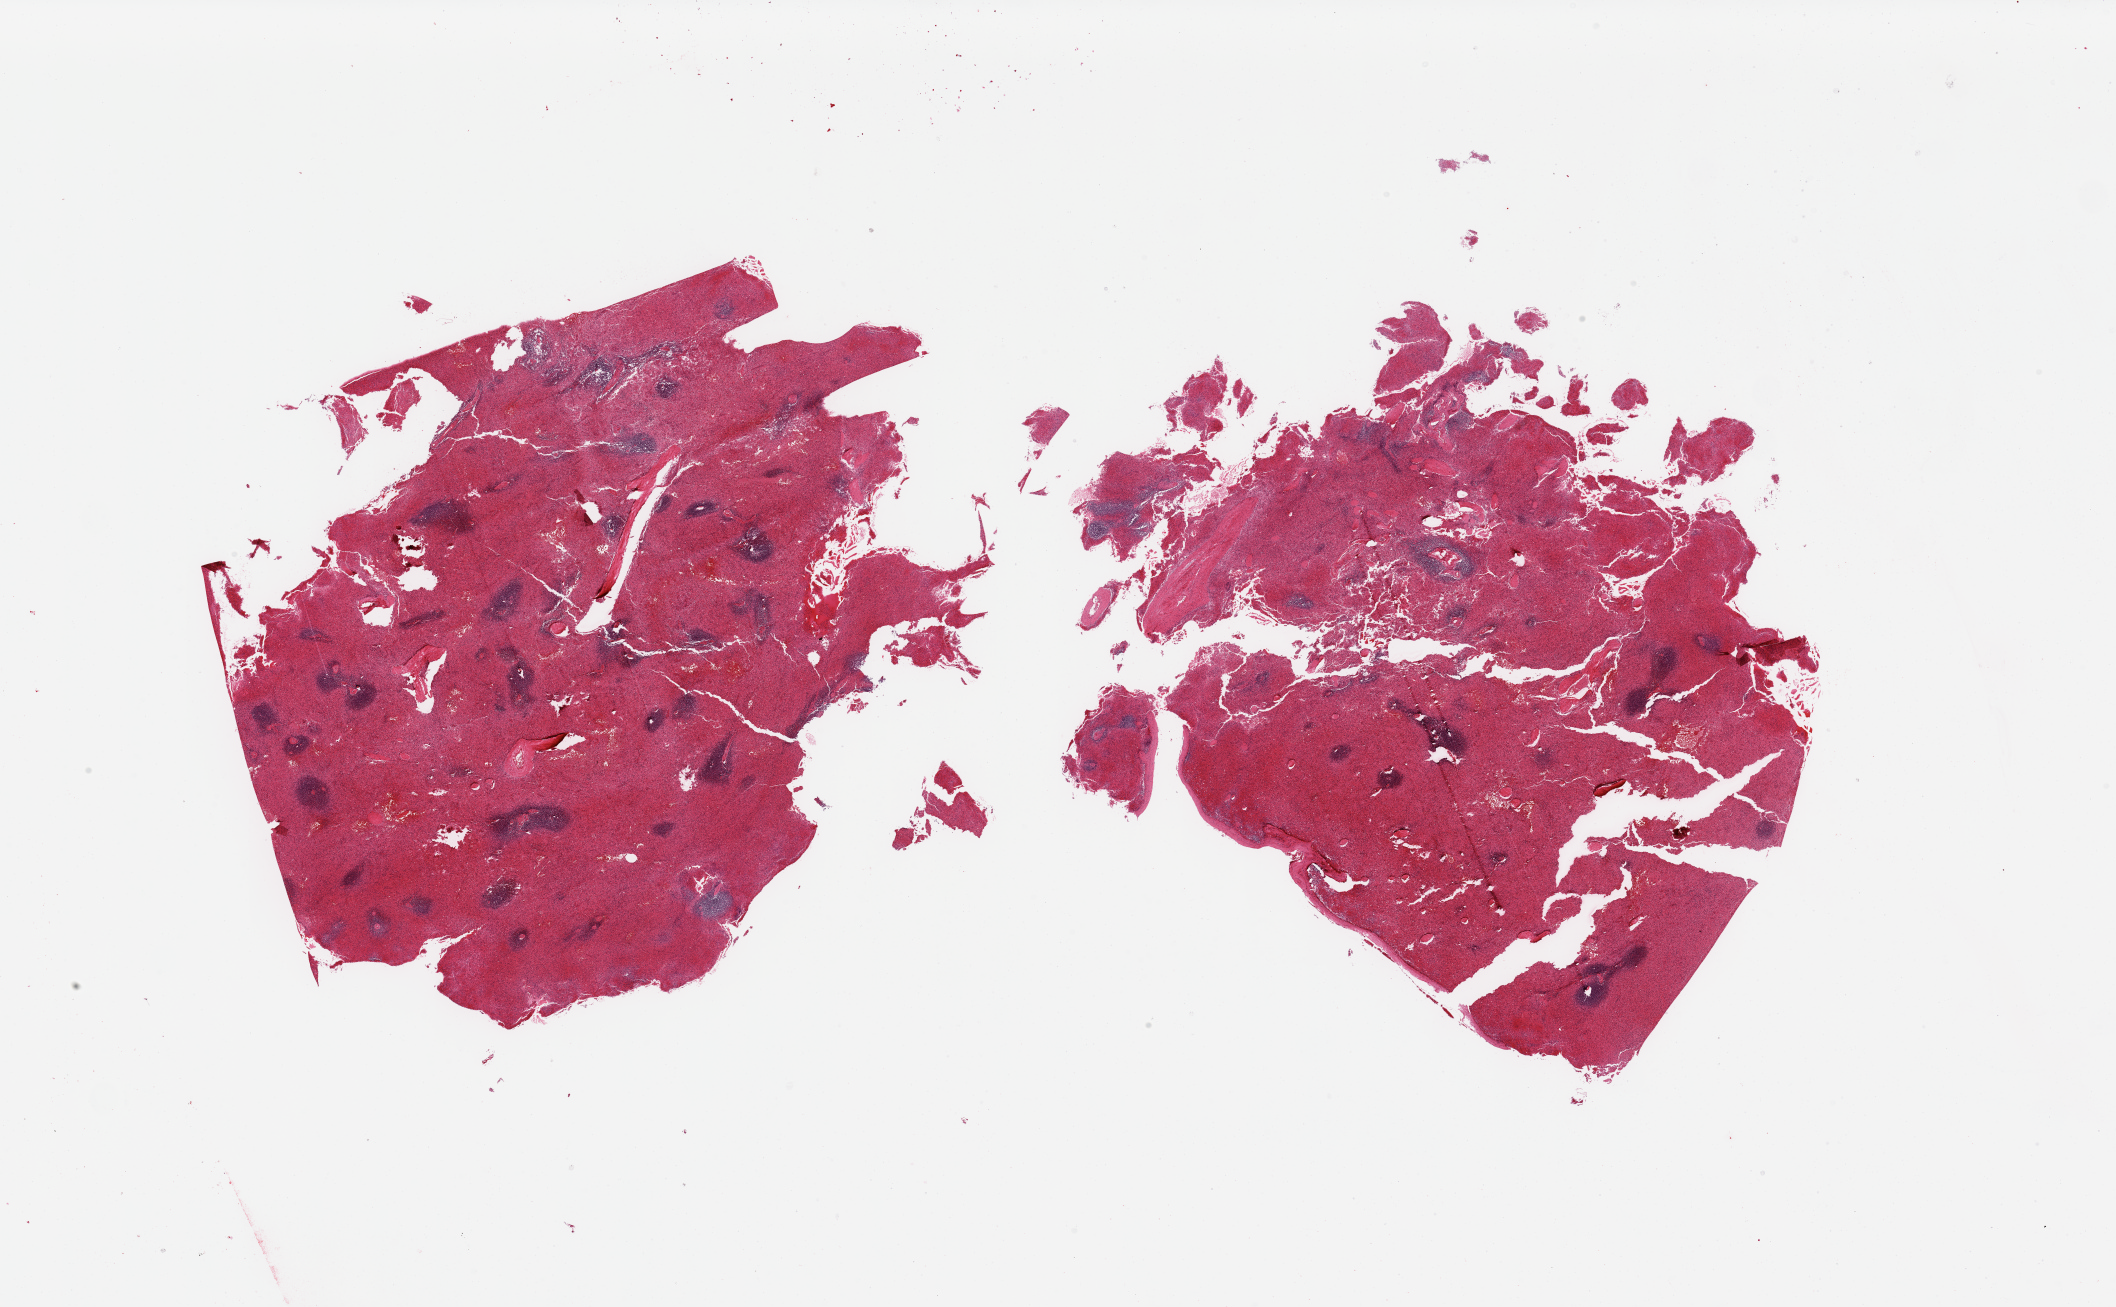
Digitized hematoxylin and eosin (H&E)-stained section — shown as a low-resolution overview of the whole scanned area (about 33.5 x 20.7 mm), PAXgene-fixed, paraffin-embedded tissue, target tissue: spleen, tissue donor sample. Donor: male.
* pathologist's review note for this sample: 2 fragmented pieces; severe congestion of red pulp